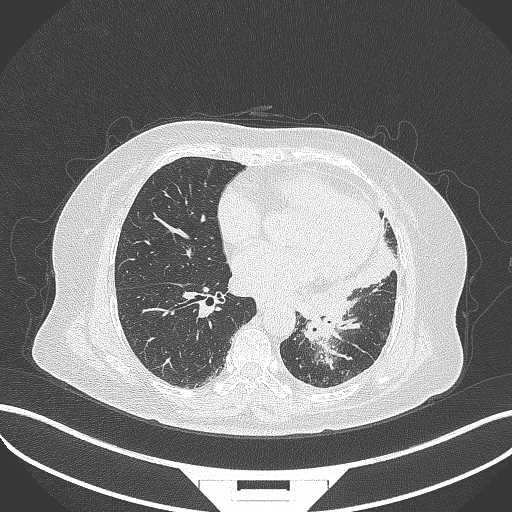
Chest CT, one axial slice; position 149 of 322 along the scan axis; reconstruction kernel B70f; lung window (W 1500 / L -600 HU); 1 mm slice thickness; 512 × 512 image matrix, field of view 400 × 400 mm. Female patient, age 69 years. From the clinical record (not read from this slice): clinical TNM (as recorded): T2b N3 M1.
Structures marked on this image (rectangle marked by the reading radiologist):
- lung tumour (recorded histology: adenocarcinoma): bounding box [x1, y1, x2, y2] px = [298, 310, 341, 346]